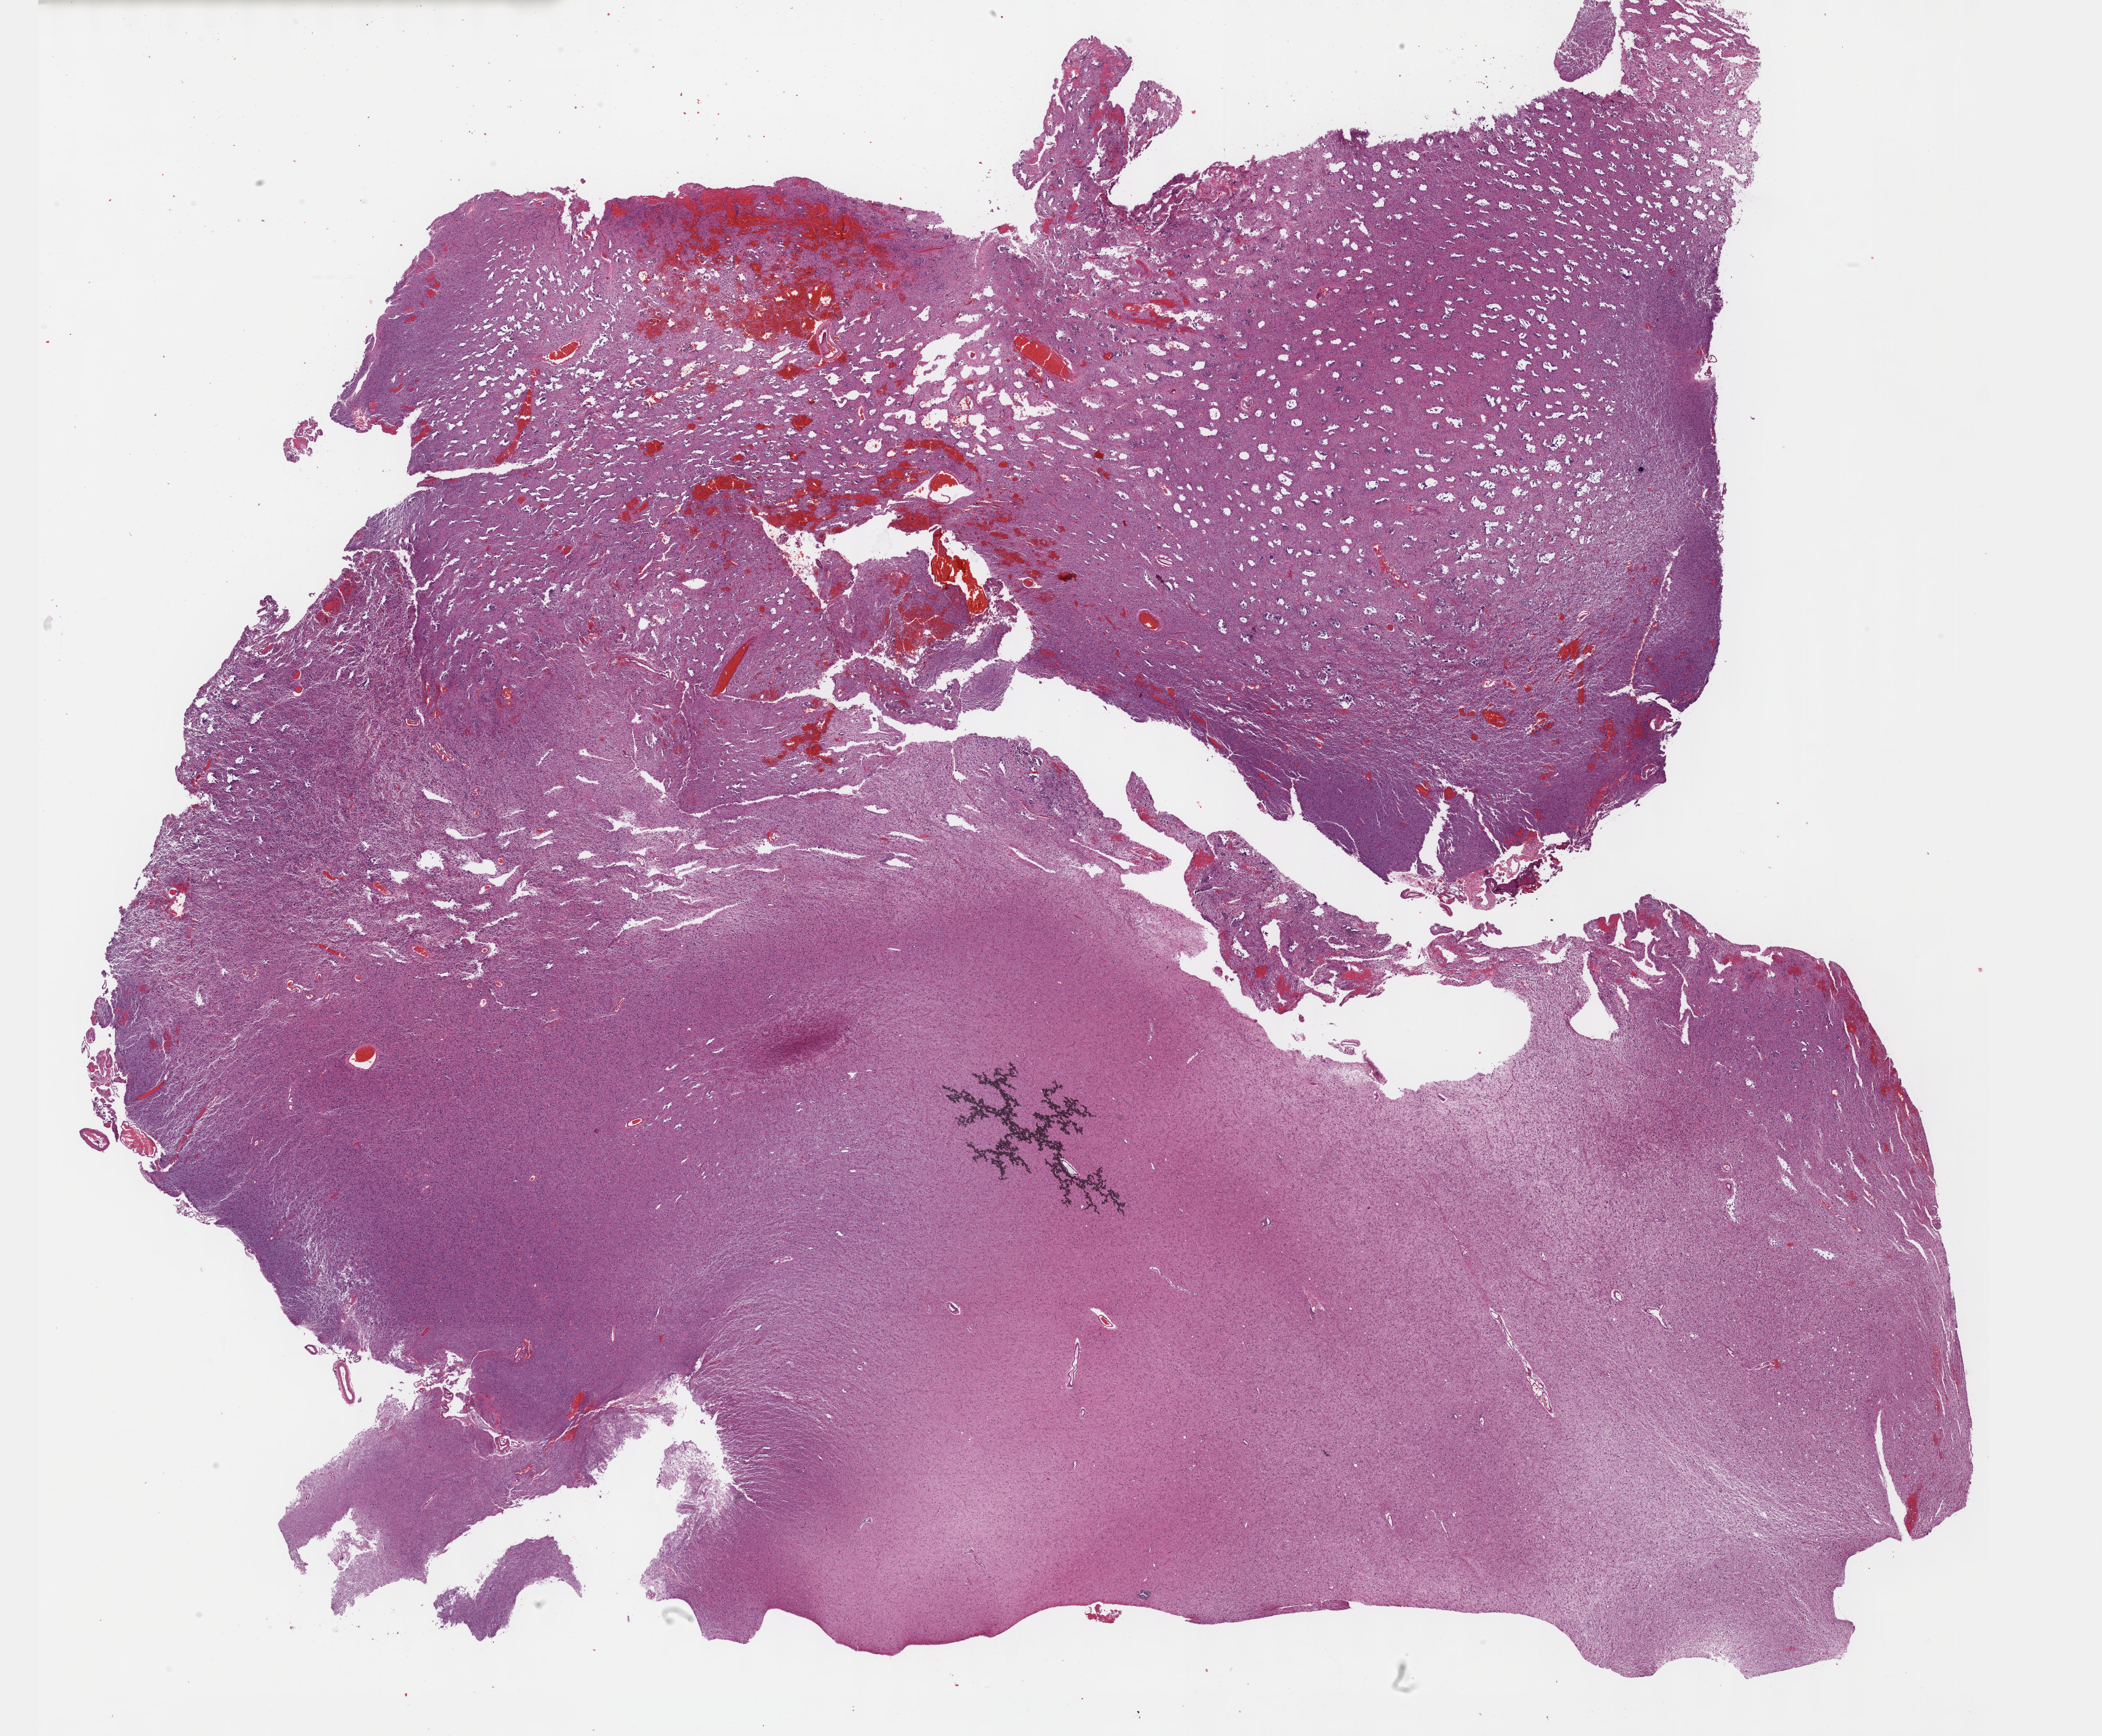
H&E whole-slide image — shown as a low-resolution overview of the whole scanned area (about 27.7 x 22.8 mm), FFPE section, primary tumour sample from the brain. Male patient; age at initial diagnosis 28 years. Histologic grade: G2 (moderately differentiated).
Histologic diagnosis: Astrocytoma, NOS. Laterality: right.